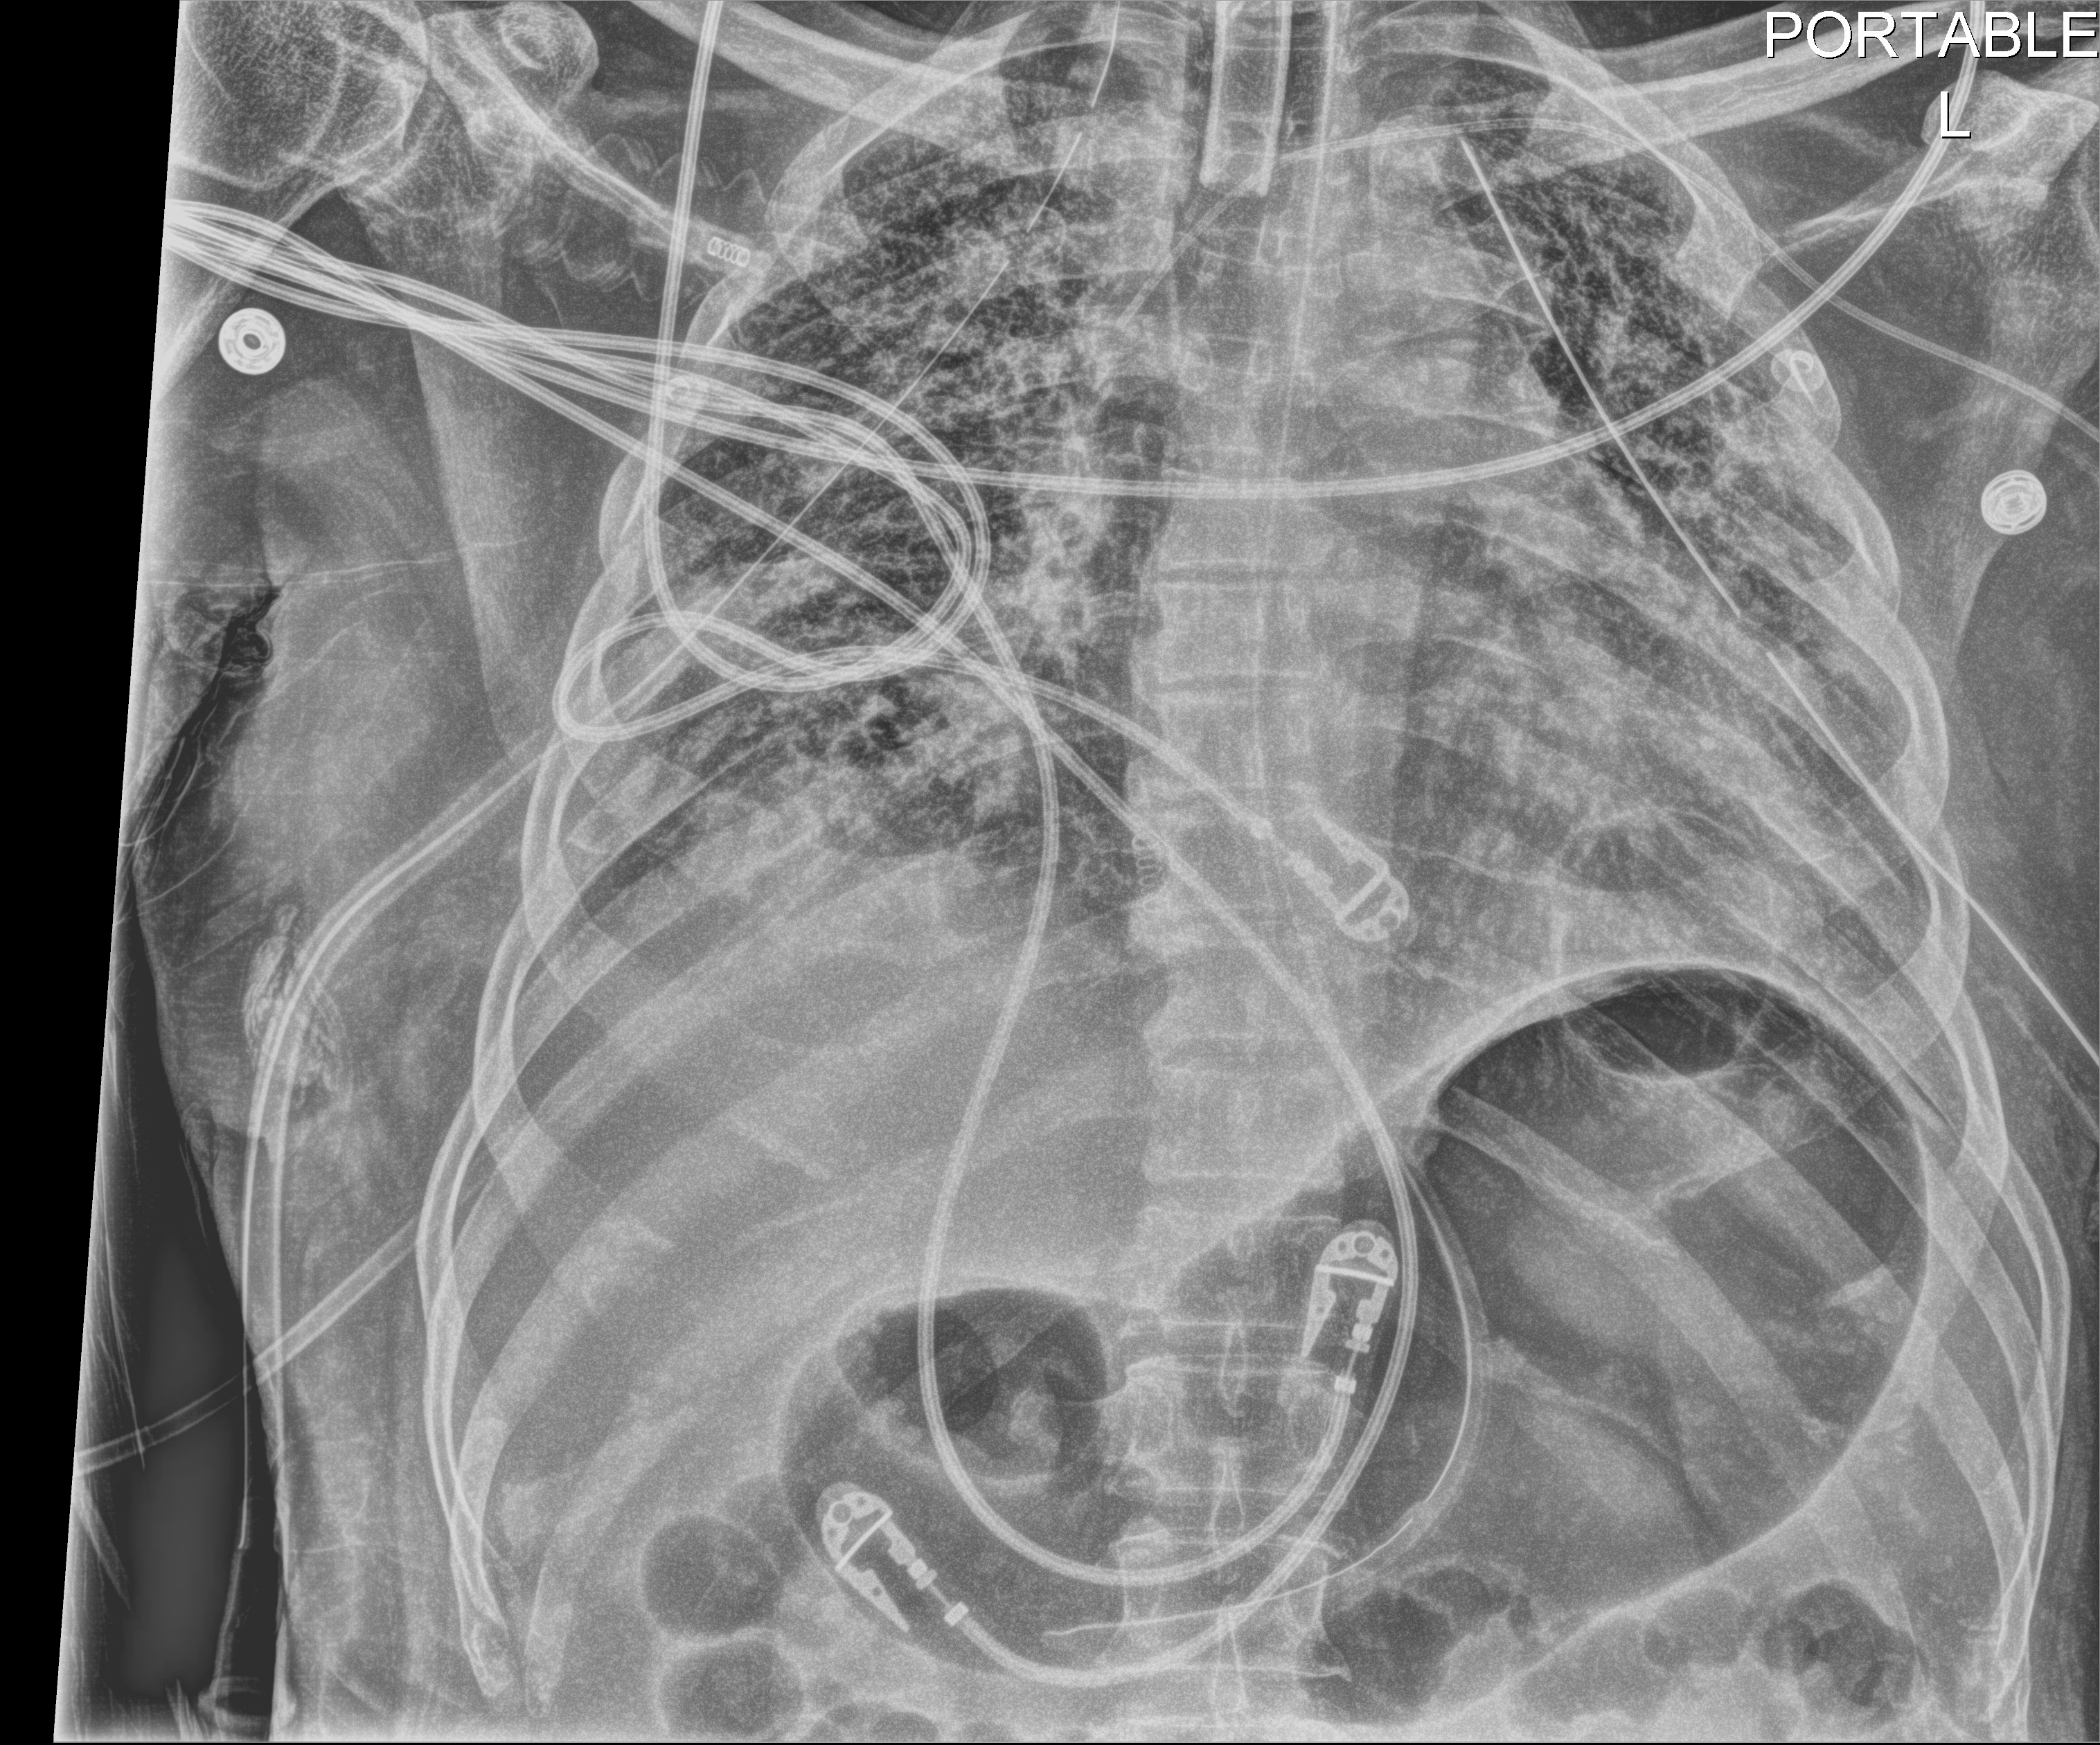
Portable chest radiograph, anteroposterior (AP) projection. Patient hospitalised with COVID-19; male, aged 18–59 years.
From the hospital-stay record, not from the radiograph (when in the stay this image was taken is not recorded): chronic kidney disease (admission record): no; length of hospital stay: 83 days.